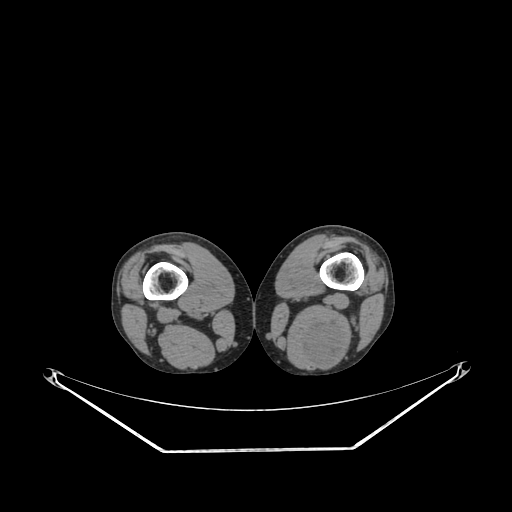
CT of an extremity soft-tissue mass (from a PET/CT study), one axial slice. Position 198 of 267 along the scan axis. Soft-tissue window (W 400 / L 40 HU). 3.75 mm slice thickness. 512 × 512 image matrix, field of view 500 × 500 mm. Male patient. Case-level facts recorded for this patient, not image findings: histological type: synovial sarcoma; site of the primary tumour: left poplietal fossa.
Structures marked on this image (expert contour drawn on MRI and transferred to this co-registered scan by the dataset authors):
- gross tumour volume (mass): bounding box (x1, y1, x2, y2) in pixels: (299, 320, 344, 364)